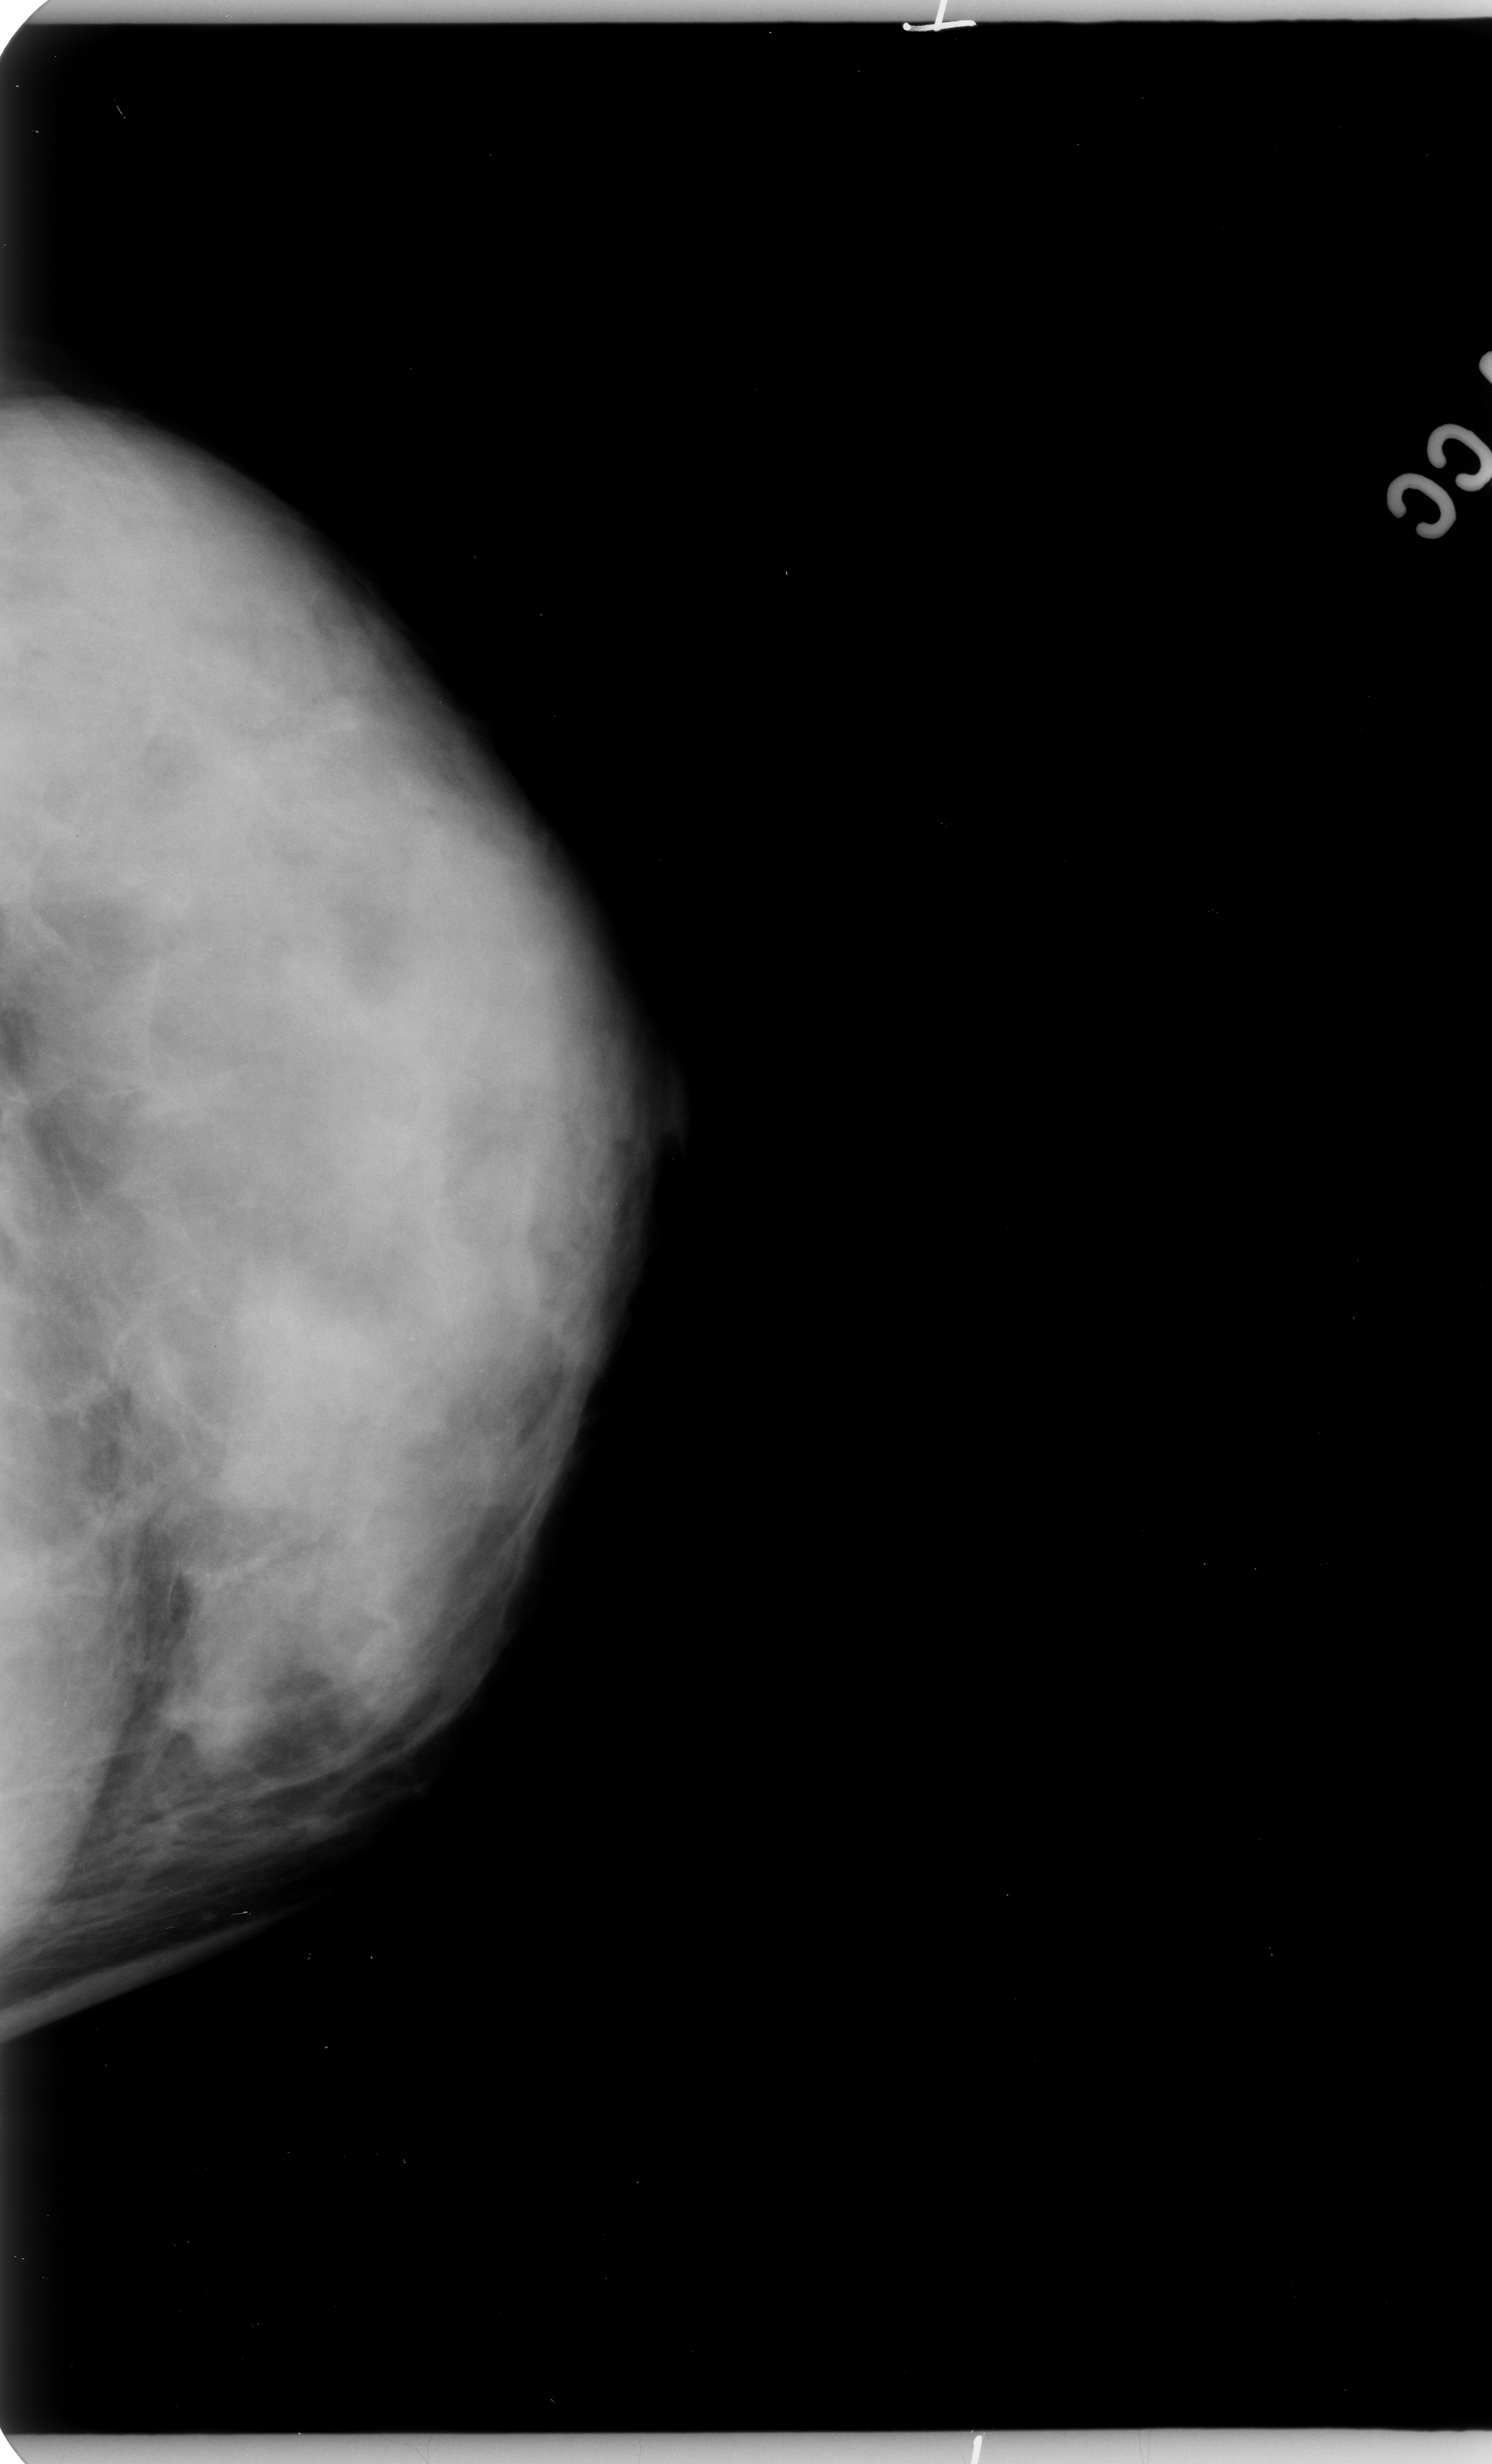
Digitized screen-film mammogram; left breast; CC view; 1492 × 2464 image matrix.
Expert-marked regions of interest on this film, with their recorded descriptors:
- calcifications, morphology pleomorphic, distribution regional; BI-RADS assessment category 4; pathology result (as recorded, not read from the image): malignant: bounding box (x1, y1, x2, y2) in pixels: (108, 1265, 257, 1627)